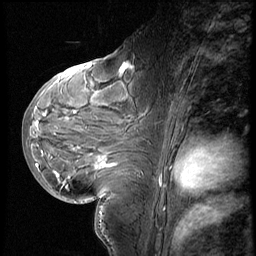
Breast MRI (dynamic contrast-enhanced), one sagittal slice. Slice 30 of 60 in the series (ordered by position). 3 images stored at this slice position (order not interpretable as contrast timing). 1.5 T. TE 4.2 ms, TR 8.9 ms. 2.5 mm slice thickness. 256 × 256 image matrix, field of view 200 × 200 mm. Patient: female, 29 years. From the clinical record (not read from this slice): setting: breast cancer imaged before/during neoadjuvant chemotherapy.
Outlined on this slice (semi-automatic segmentation, software-assisted and operator-edited):
- analysis volume of interest (the breast-tissue region the enhancement analysis was run in; not a lesion): bounding box [x1, y1, x2, y2] px = [29, 57, 152, 200]
- tumour enhancement mask (voxels above the 140 % enhancement threshold inside the analysis volume of interest): [37, 64, 129, 169]